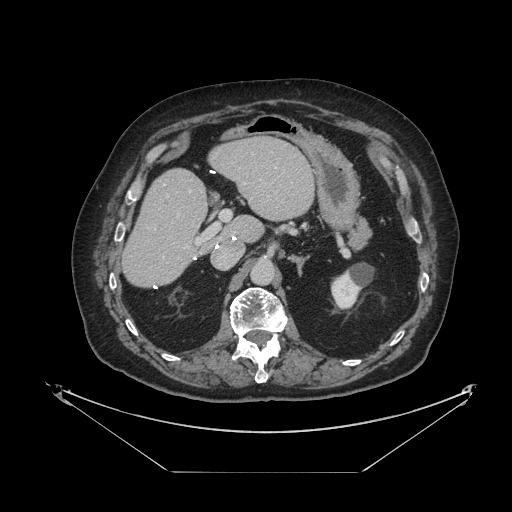
Contrast-enhanced abdominal CT, one axial slice; position 57 of 121 along the scan axis; intravenous contrast given; soft-tissue window (W 400 / L 40 HU); 512 × 512 image matrix, field of view 500 × 500 mm. Male patient, age 68 years. Case-level facts recorded for this patient, not image findings: diagnosis: colorectal cancer liver metastases, imaged before liver resection; multiple liver metastases: no; largest metastasis: 4 cm; disease in both lobes: no.
Structures marked on this image (expert manual segmentation):
- hepatic veins: bounding box [x1, y1, x2, y2] px = [163, 167, 276, 259]
- liver: [123, 138, 315, 287]
- planned liver remnant (the part of the liver to remain after resection): [123, 138, 315, 287]
- portal vein (with intrahepatic branches): [167, 196, 231, 248]